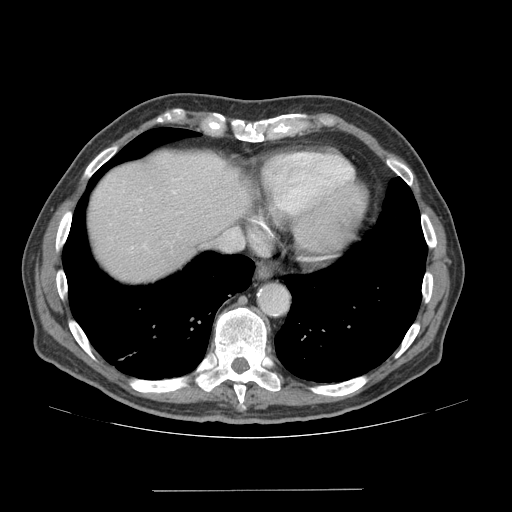
Contrast-enhanced abdominal CT (liver protocol), one axial slice; slice 63 of 77 in the series (ordered by position); reconstruction kernel STANDARD; soft-tissue window (W 400 / L 40 HU); 2.5 mm slice thickness; 512 × 512 image matrix. Case-level facts recorded for this patient, not image findings: diagnosis: hepatocellular carcinoma (patient treated with transarterial chemoembolisation; whether this scan precedes or follows treatment is not stated here); TNM stage (as recorded): Stage-IVA; Child-Pugh class: A; tumour nodularity: uninodular.
Outlined on this slice (semi-automatic segmentation, software-assisted and operator-edited):
- abdominal aorta: box from (x=258, y=285) to (x=287, y=313) px
- liver parenchyma outside the tumour (the mass and vessels are separate outlines, so this box may not span the whole liver): (x=88, y=150)–(x=250, y=282)
- liver vessels: (x=140, y=191)–(x=176, y=210)